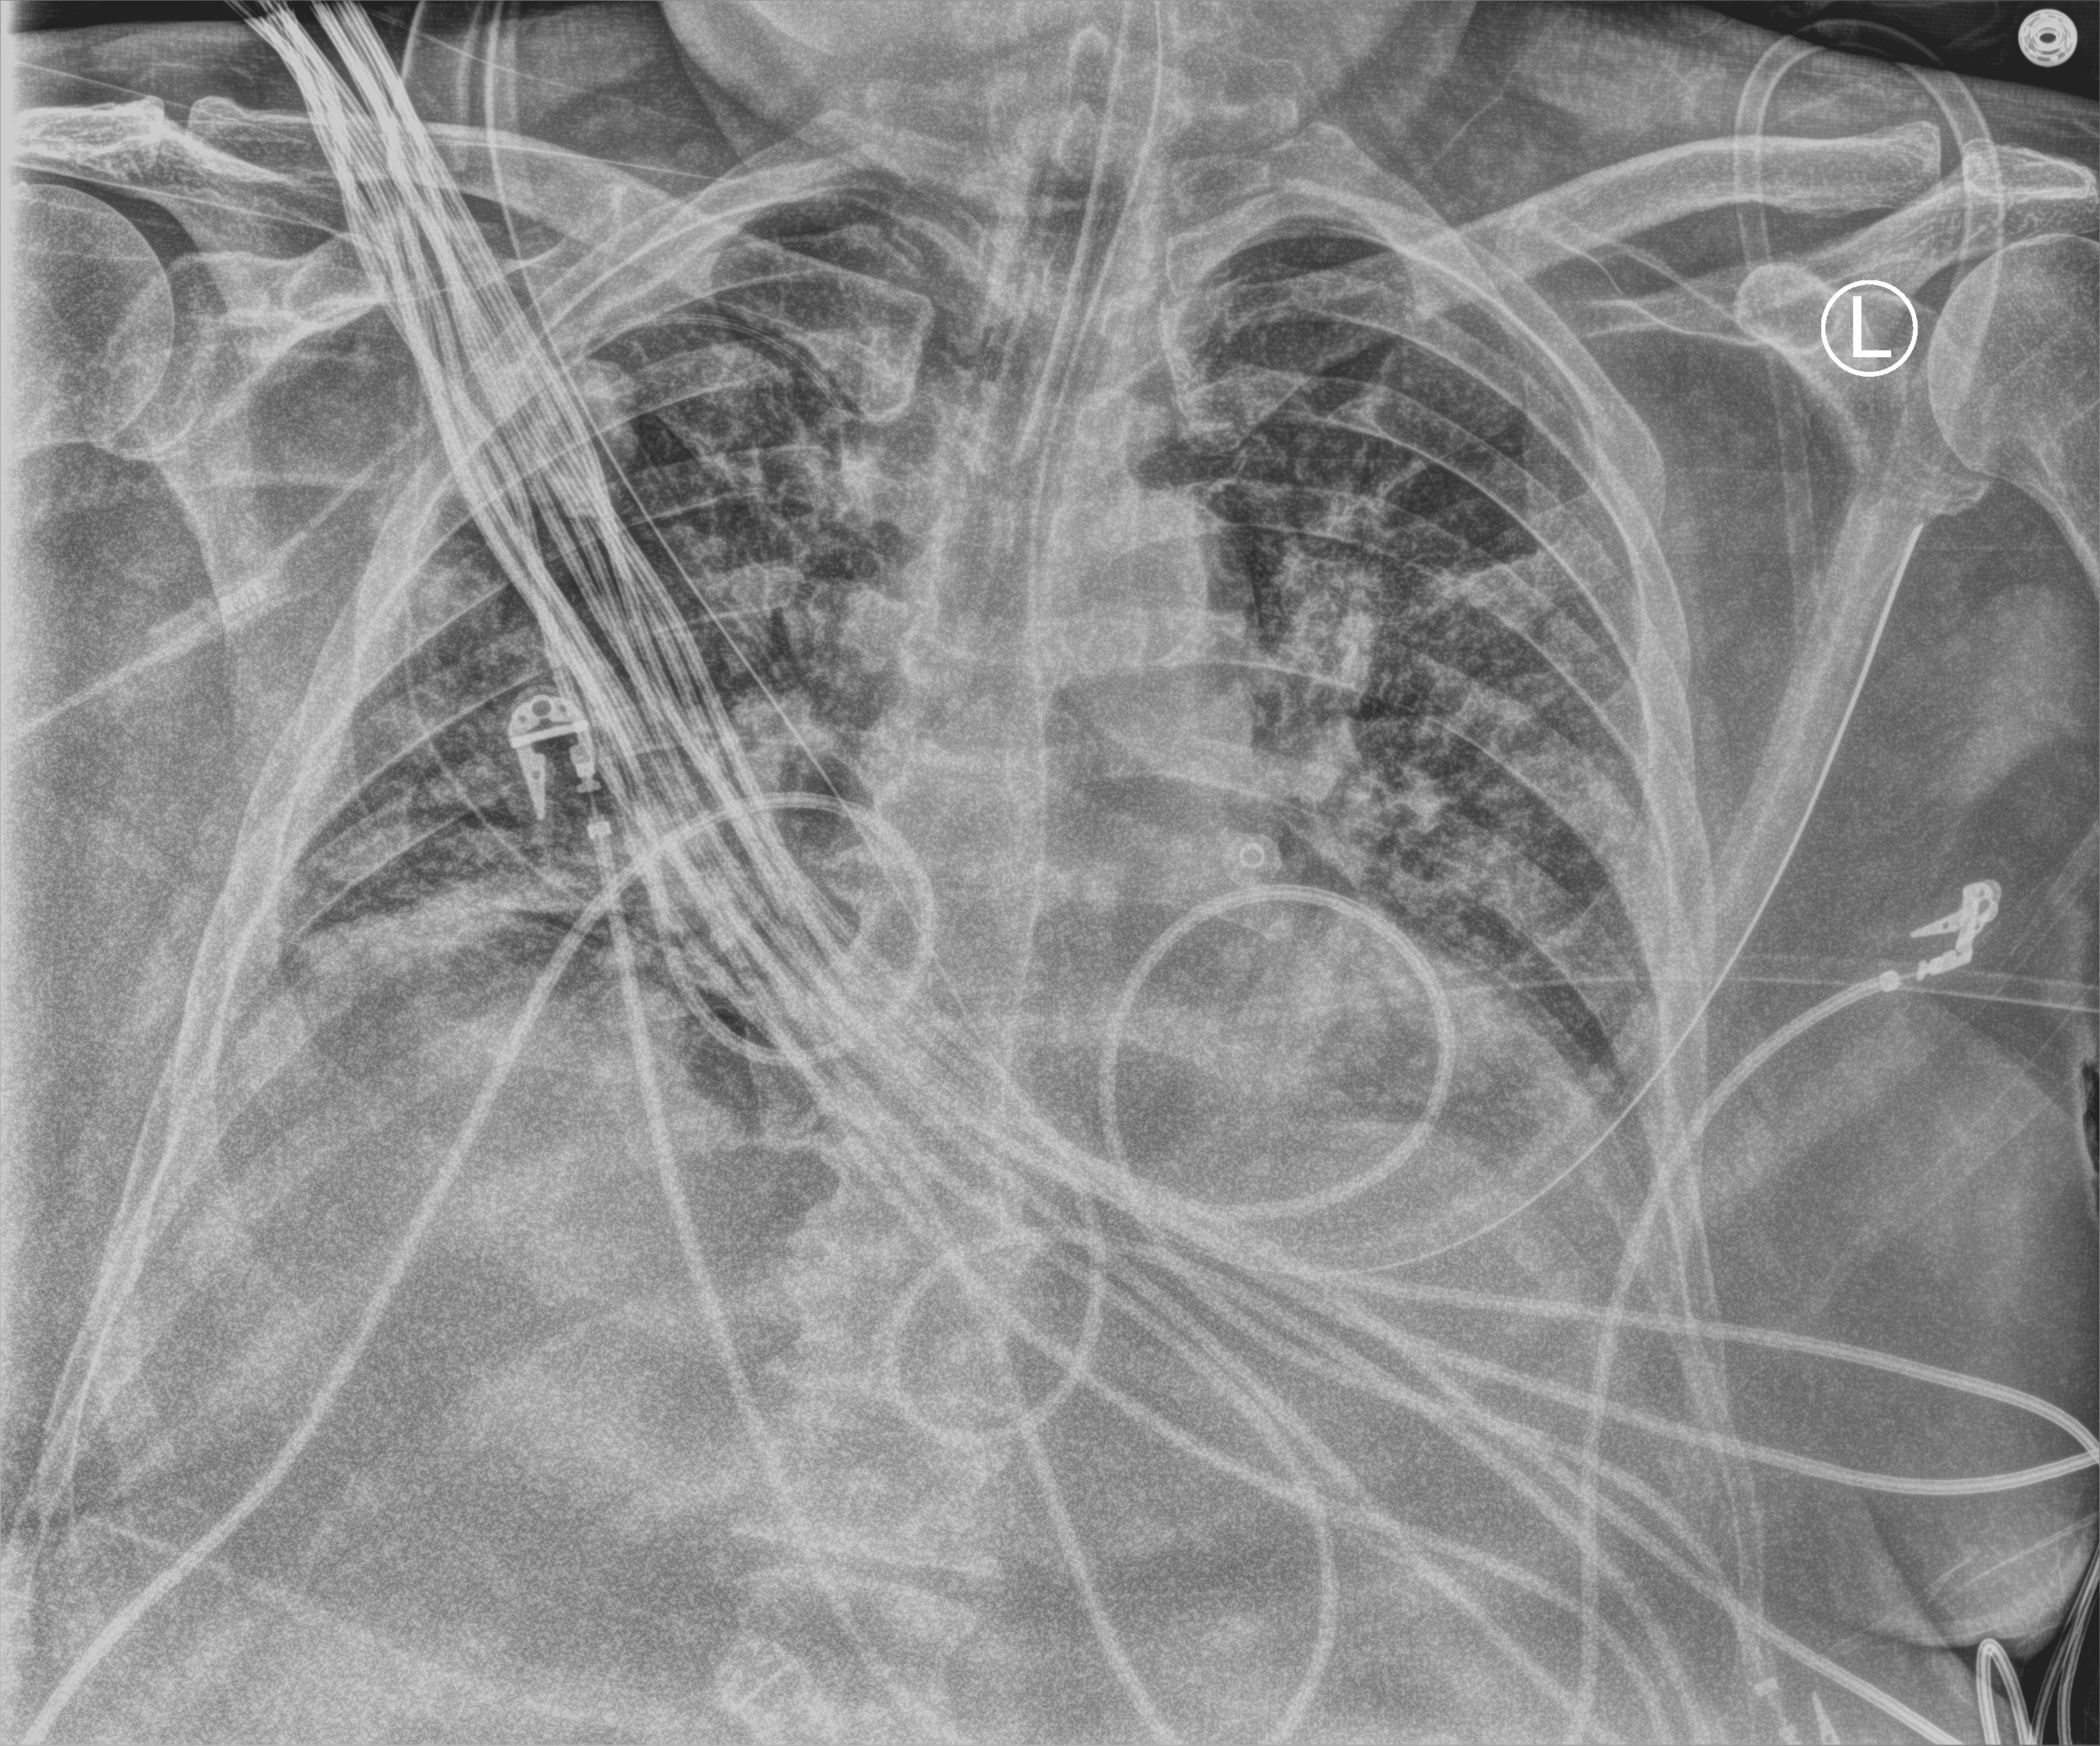
Portable chest radiograph, anteroposterior (AP) projection. Patient hospitalised with COVID-19; male, aged 60–74 years.
From the hospital-stay record, not from the radiograph (when in the stay this image was taken is not recorded): admitted to intensive care during this hospital stay: yes; length of hospital stay: 26 days; mechanically ventilated during this hospital stay: yes.